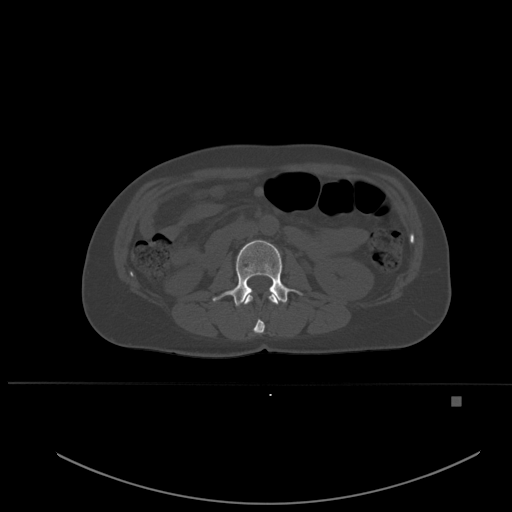
CT including the spine, one axial slice; position 218 of 651 along the scan axis; bone window (W 1800 / L 400 HU); 1.5 mm slice thickness; 512 × 512 image matrix, field of view 443 × 443 mm. Patient: female, 49 years. From the clinical record (not read from this slice): primary cancer: breast.
Structures marked on this image (semi-automatically segmented with operator editing):
- L1 vertebra: bounding box (x1, y1, x2, y2) in pixels: (243, 294, 279, 334)
- L2 vertebra: (213, 240, 303, 307)